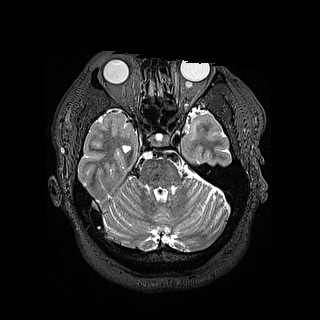
Brain MRI from a brain-tumour surgery series, one axial slice. 1.2 mm slice thickness. 320 × 320 image matrix. Case-level facts recorded for this patient, not image findings: histopathology: Astrocytoma; WHO grade: 2; IDH mutation: yes.
Outlined on this slice (expert manual segmentation):
- tumour: box from (x=188, y=126) to (x=198, y=140) px